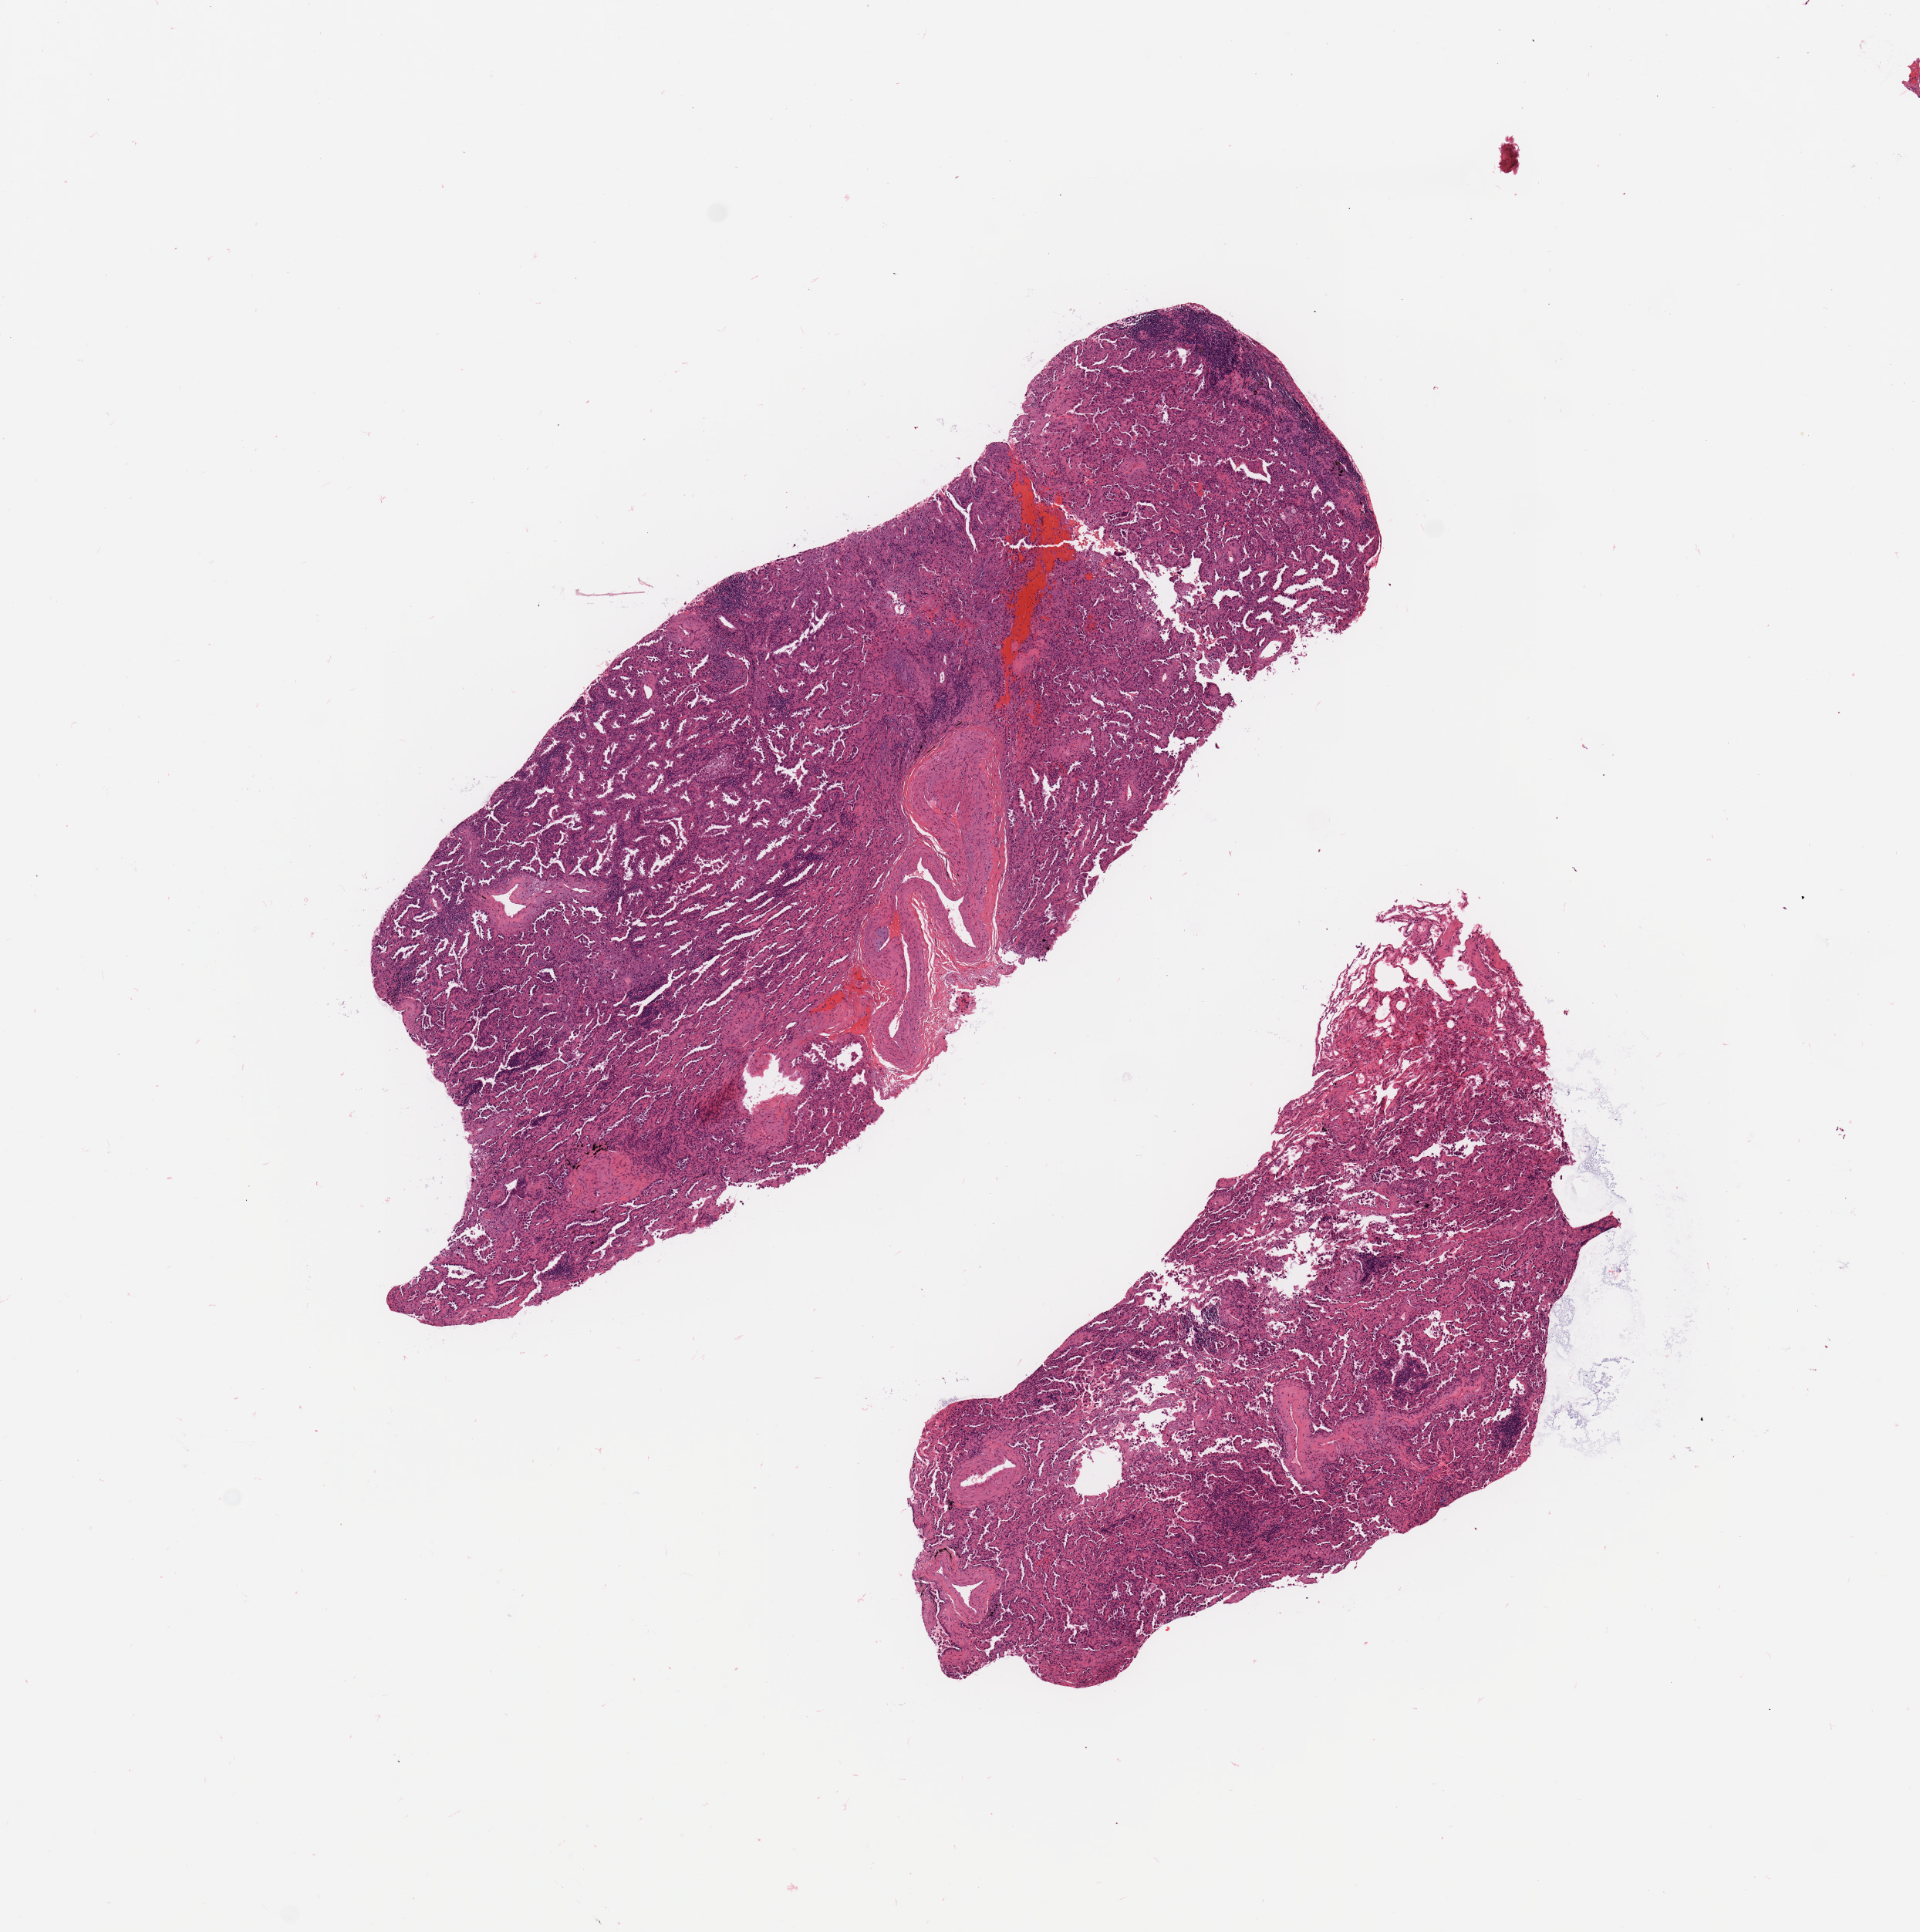
Hematoxylin and eosin (H&E) stained whole-slide image, whole scanned area (about 9.8 x 9.9 mm, acquisition: 20x scan) shown as a low-resolution overview. Tumour tissue sample, sampled site: lung. Patient: female, age 70 years. Histologic grade: GX (grade cannot be assessed). Composition of this section per pathologist review: tumour nuclei 70%, necrosis 3%.
Histologic diagnosis: Adenocarcinoma, NOS. AJCC pathologic stage: IB.